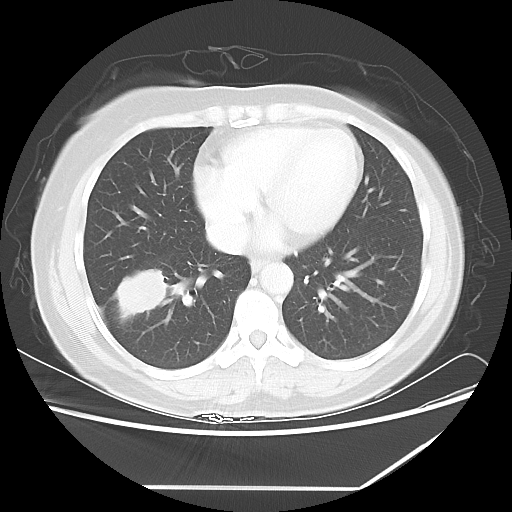
Chest CT, one axial slice; slice 24 of 60 in the series (ordered by position); reconstruction kernel LUNG; lung window (W 1500 / L -600 HU); 512 × 512 image matrix, field of view 374 × 374 mm. Patient: female, 42 years. From the clinical record (not read from this slice): clinical TNM (as recorded): T2 N1 M0.
Structures marked on this image (bounding box drawn by a radiologist):
- lung tumour (recorded histology: adenocarcinoma): bounding box (x1, y1, x2, y2) in pixels: (112, 263, 171, 326)